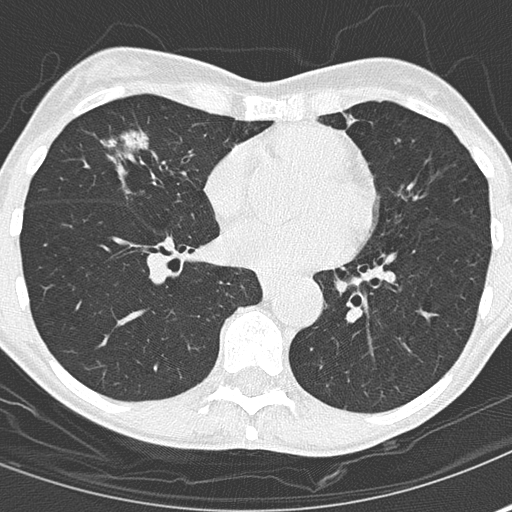
Chest CT (low-dose screening protocol), one axial image; second annual screen; lung window (W 1500 / L -600 HU); 2 mm slice thickness; lung (sharp) reconstruction kernel (B50f); slice 100 of 167 in the series; 512 × 512 image matrix. Female, age 67 years at enrolment.
Expert-annotated lung lesion, bounding box (x1, y1, x2, y2) in pixels: (83, 117, 184, 207). The screening reader recorded 2 non-calcified nodules or masses ≥4 mm on this exam (right middle lobe, right middle lobe); which of them this box marks is not recorded.